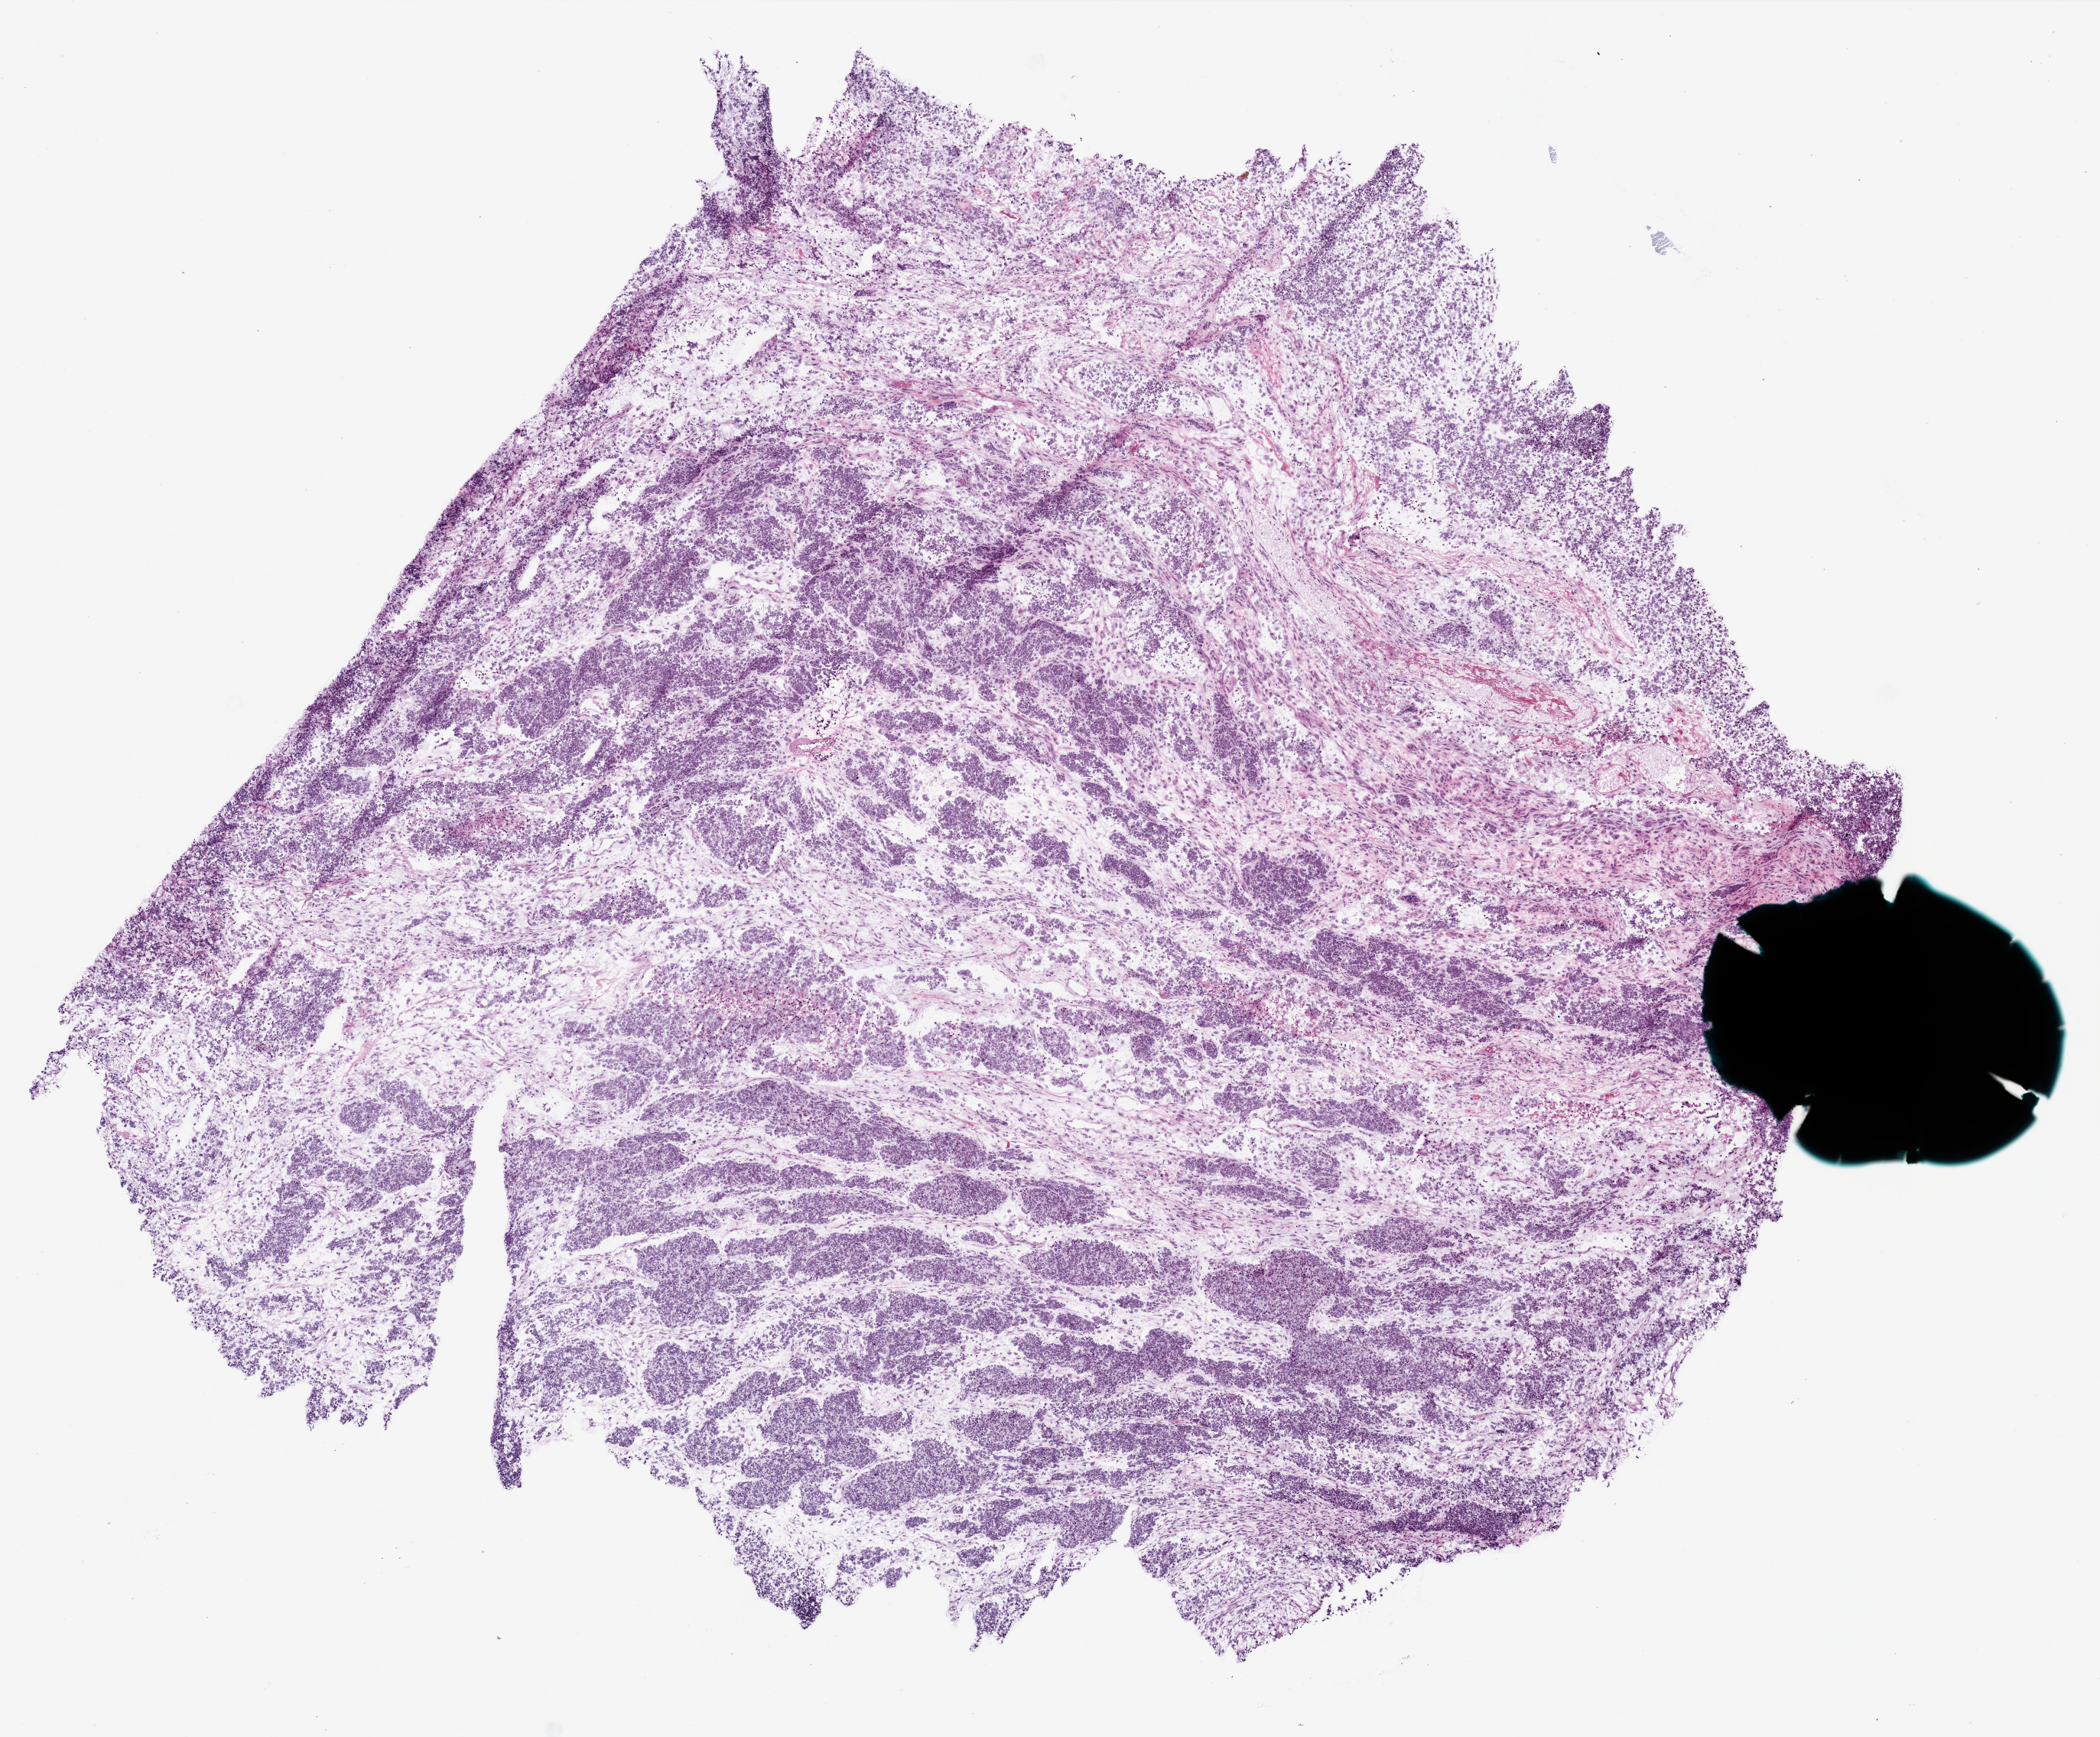
Whole-slide histology image, Hematoxylin and eosin (H&E) stained, whole scanned area (about 11.0 x 9.1 mm, slide scanned at 20x) shown as a low-resolution overview, frozen section from the bottom of the tissue portion, sample: primary tumour, brain. Patient: male, age at initial diagnosis 75 years. Composition of this section per pathologist review: tumour cells 95%, tumour nuclei 95%, normal cells 0%, stromal cells 5%, necrosis 0%.
Histologic diagnosis: Glioblastoma.